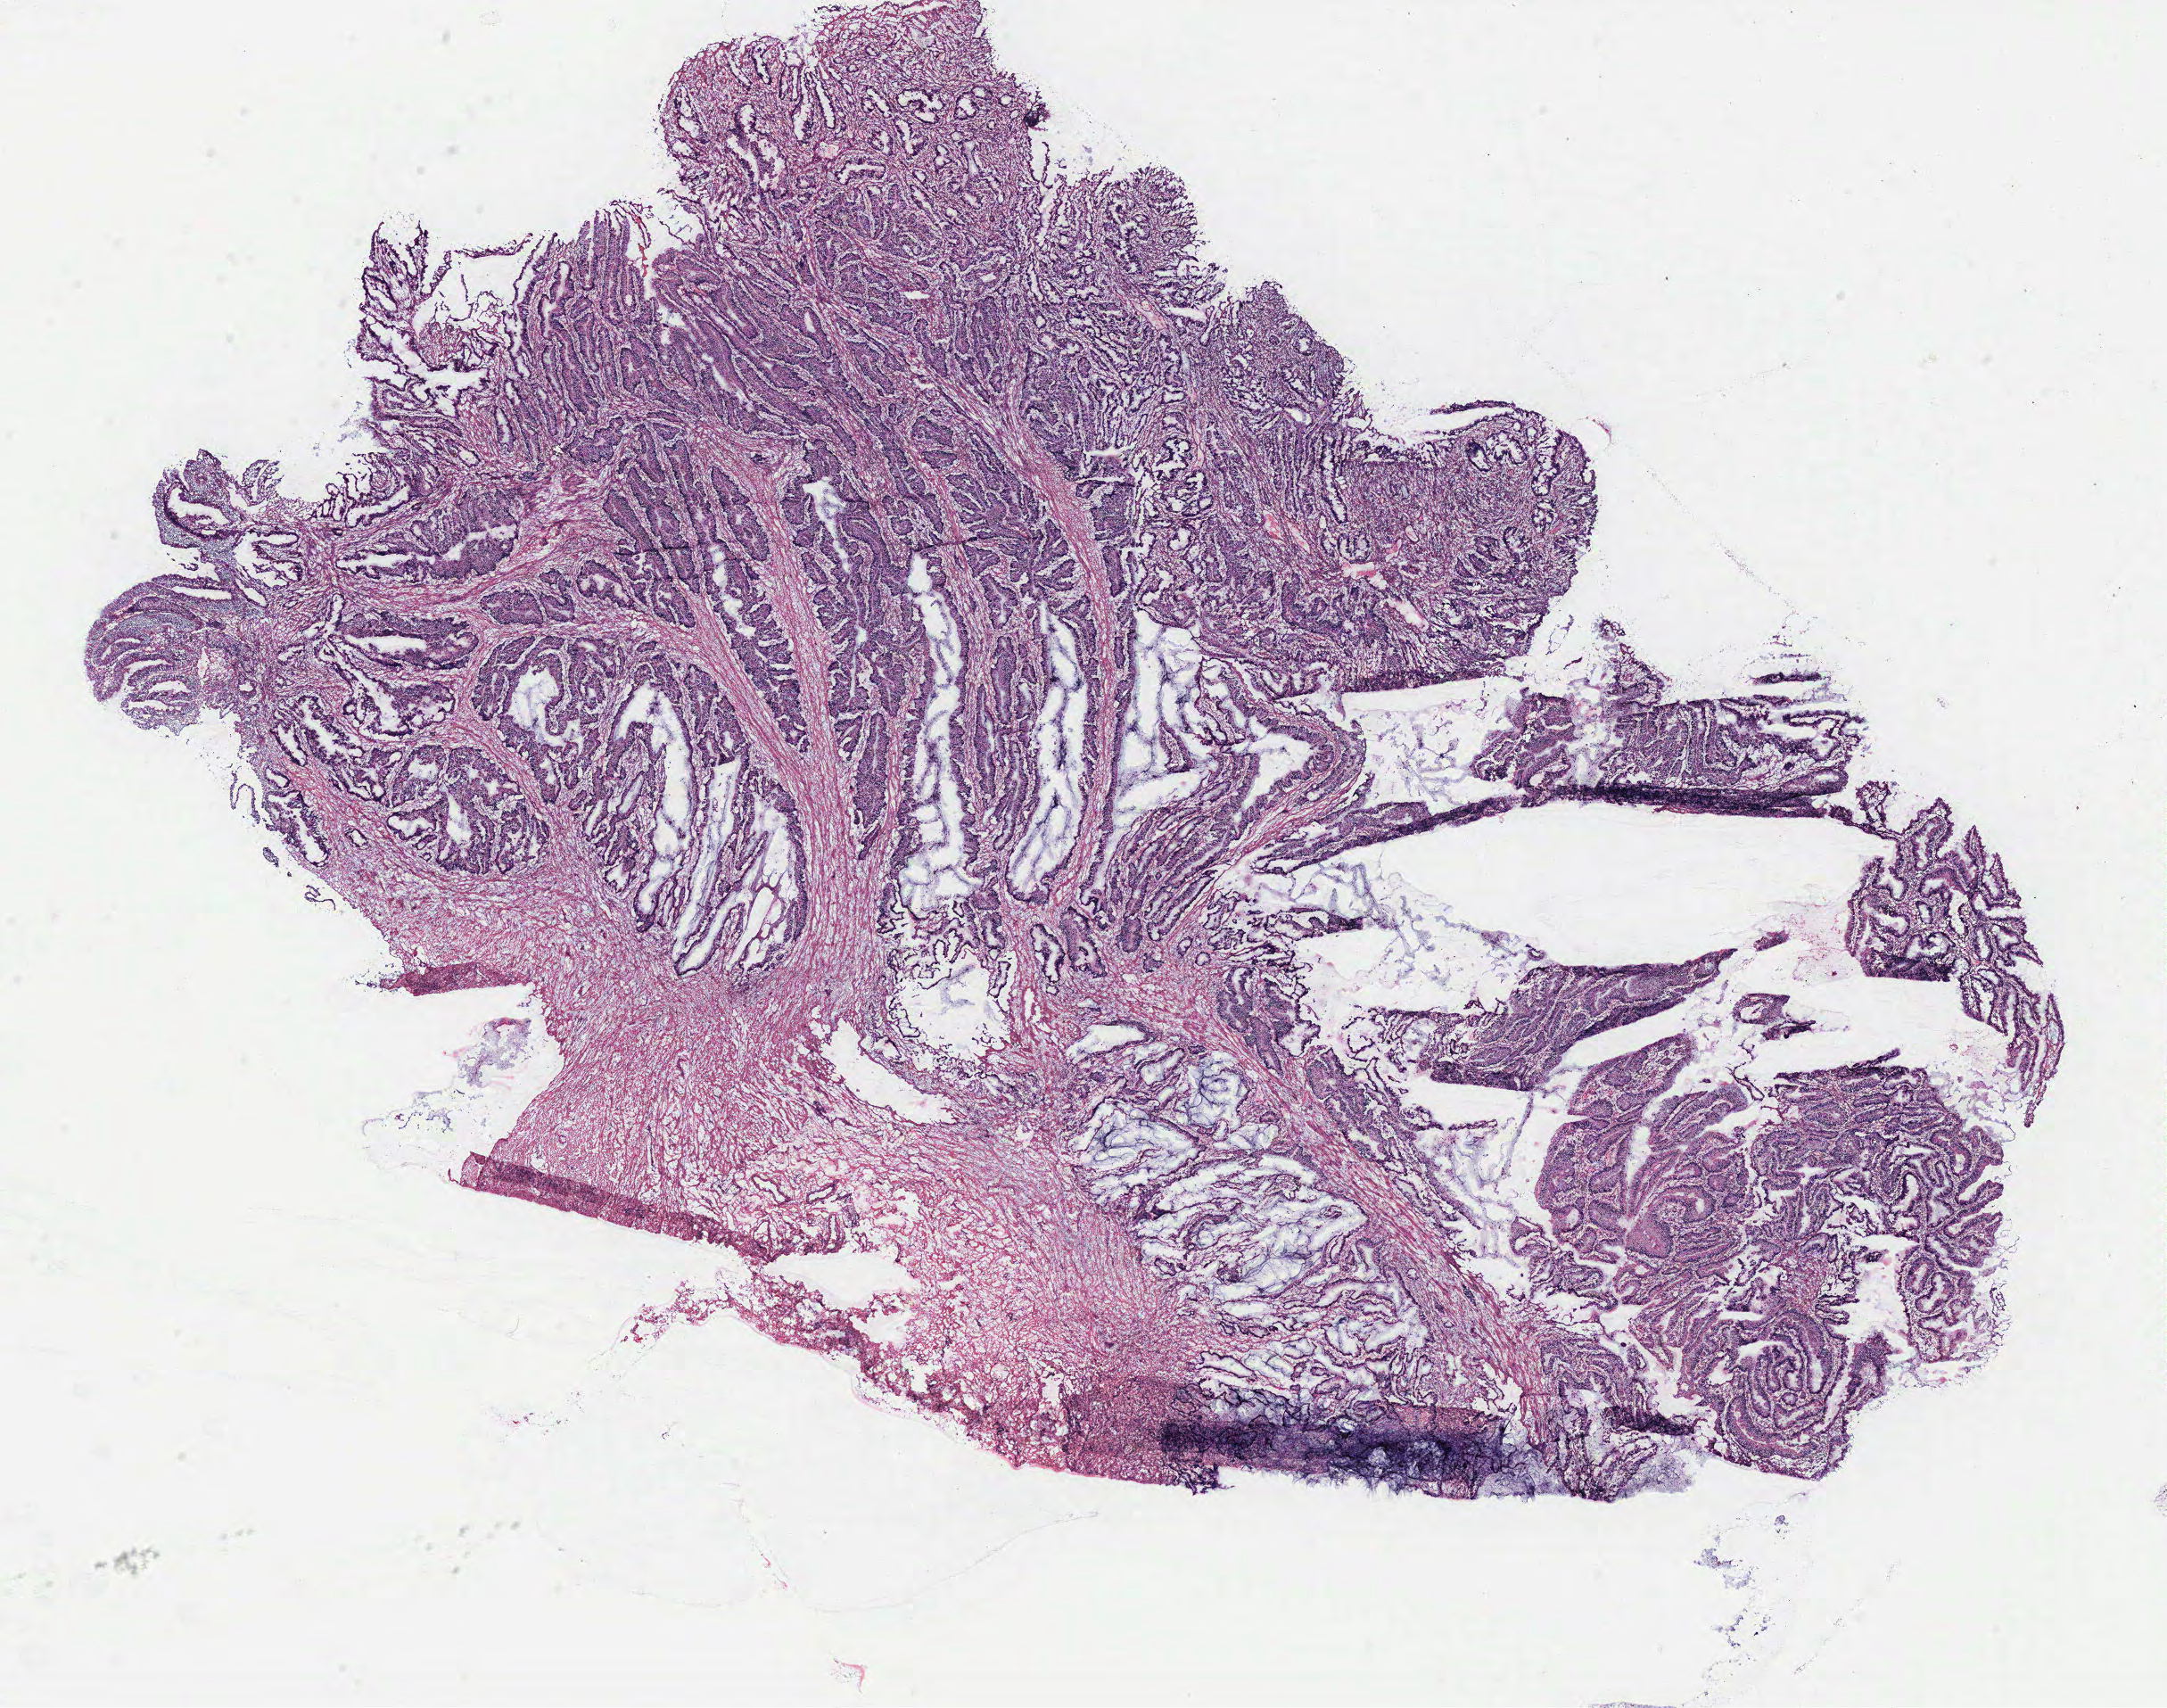
Whole-slide histology image, H&E — shown as a low-resolution overview of the whole scanned area (about 19.4 x 15.3 mm), colon, normal (non-tumour) tissue. 55-year-old male patient.
This section: normal (non-tumour) tissue from the same patient. Patient diagnosis: Adenocarcinoma, NOS.